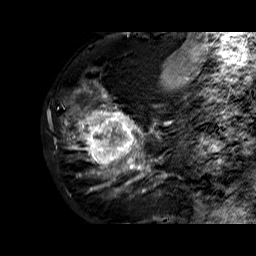
Breast MRI (dynamic contrast-enhanced), one sagittal slice. Position 23 of 60 along the scan axis. Dynamic contrast-enhanced series, time point 2 of 6 at this slice position (early post-contrast). 1.5 T. TE 6.3 ms, TR 32.4 ms. 4 mm slice thickness. 256 × 256 image matrix, field of view 200 × 200 mm. Female patient. Case-level facts recorded for this patient, not image findings: setting: breast cancer imaged before/during neoadjuvant chemotherapy; receptor status: HR-positive, HER2-negative.
Annotated regions visible in this slice (semi-automatic segmentation, software-assisted and operator-edited):
- analysis volume of interest (the breast-tissue region the enhancement analysis was run in; not a lesion): bounding box [x1, y1, x2, y2] px = [68, 72, 177, 183]
- tumour enhancement mask (voxels above the 100 % enhancement threshold inside the analysis volume of interest): [79, 93, 168, 183]